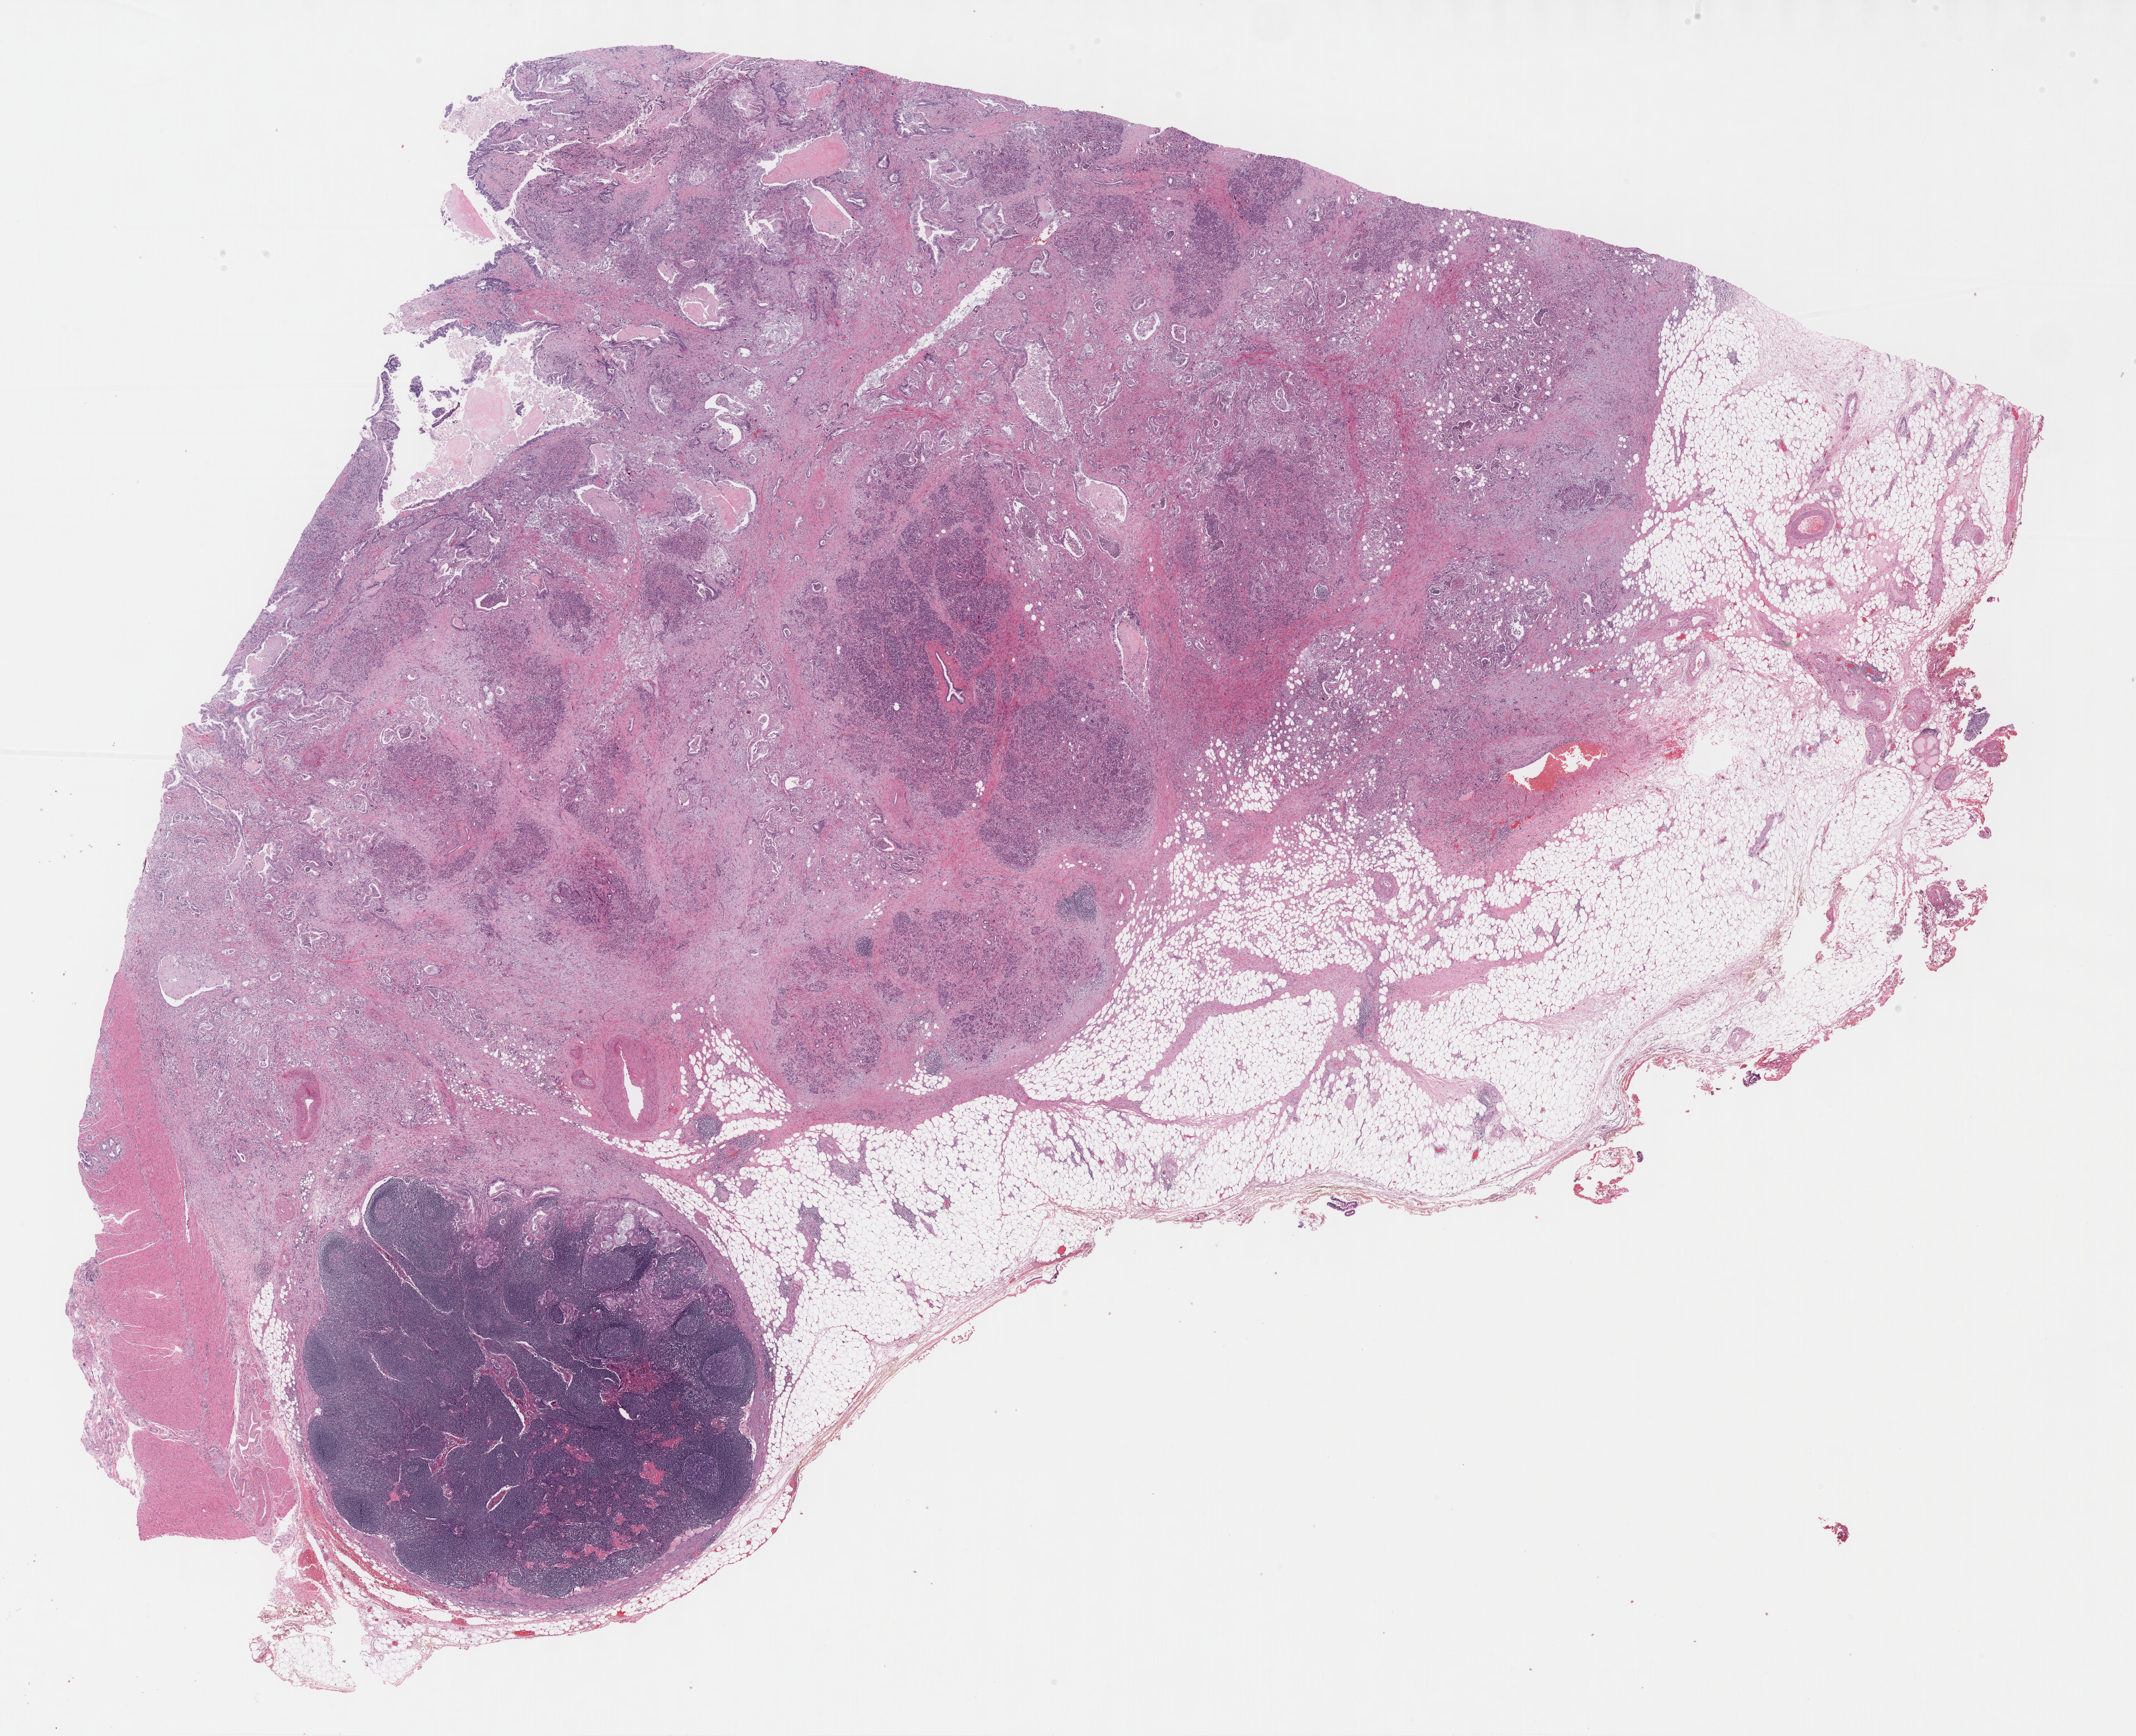
Whole-slide histology image, H&E-stained — shown as a low-resolution overview of the whole scanned area (about 26.2 x 21.3 mm, acquisition: 40x scan); formalin-fixed paraffin-embedded (FFPE) diagnostic section; sample: primary tumour, pancreas. Female patient; age at initial diagnosis 73 years. Histologic grade: G2 (moderately differentiated).
AJCC pathologic stage: IIB. Pathologic diagnosis: Infiltrating duct carcinoma, NOS (head of pancreas). Lymph nodes positive (case pathology): 5 of 13 examined.